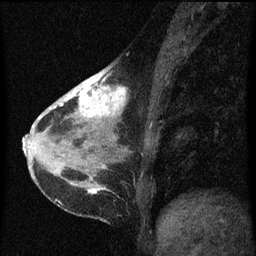
Breast MRI (dynamic contrast-enhanced), one sagittal slice. Position 25 of 60 along the scan axis. Dynamic contrast-enhanced series, image 2 of 3 at this slice position (ordered by acquisition). 1.5 T. TE 4.2 ms, TR 8 ms. 2 mm slice thickness. 256 × 256 image matrix, field of view 180 × 180 mm. Female patient, age 38 years.
Outlined on this slice (semi-automatically segmented with operator editing):
- analysis volume of interest (the breast-tissue region the enhancement analysis was run in; not a lesion): box from (x=61, y=66) to (x=129, y=147) px
- tumour enhancement mask (voxels above the 70 % enhancement threshold inside the analysis volume of interest): (x=61, y=68)–(x=128, y=139)